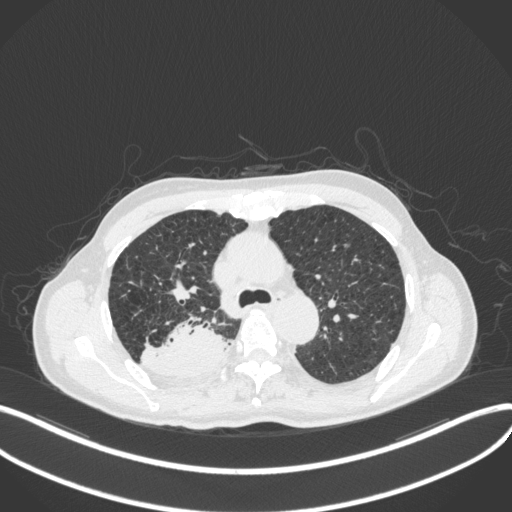
Chest CT, one axial slice; slice 313 of 423 in the series (ordered by position); reconstruction kernel B31f; 120 kVp; lung window (W 1500 / L -600 HU); 1 mm slice thickness; 512 × 512 image matrix, field of view 400 × 400 mm. Male patient, age 79 years. Case-level facts recorded for this patient, not image findings: clinical TNM (as recorded): T3 N0 M0.
Structures marked on this image (rectangle marked by the reading radiologist):
- lung tumour (recorded histology: adenocarcinoma): box from (x=138, y=309) to (x=230, y=380) px